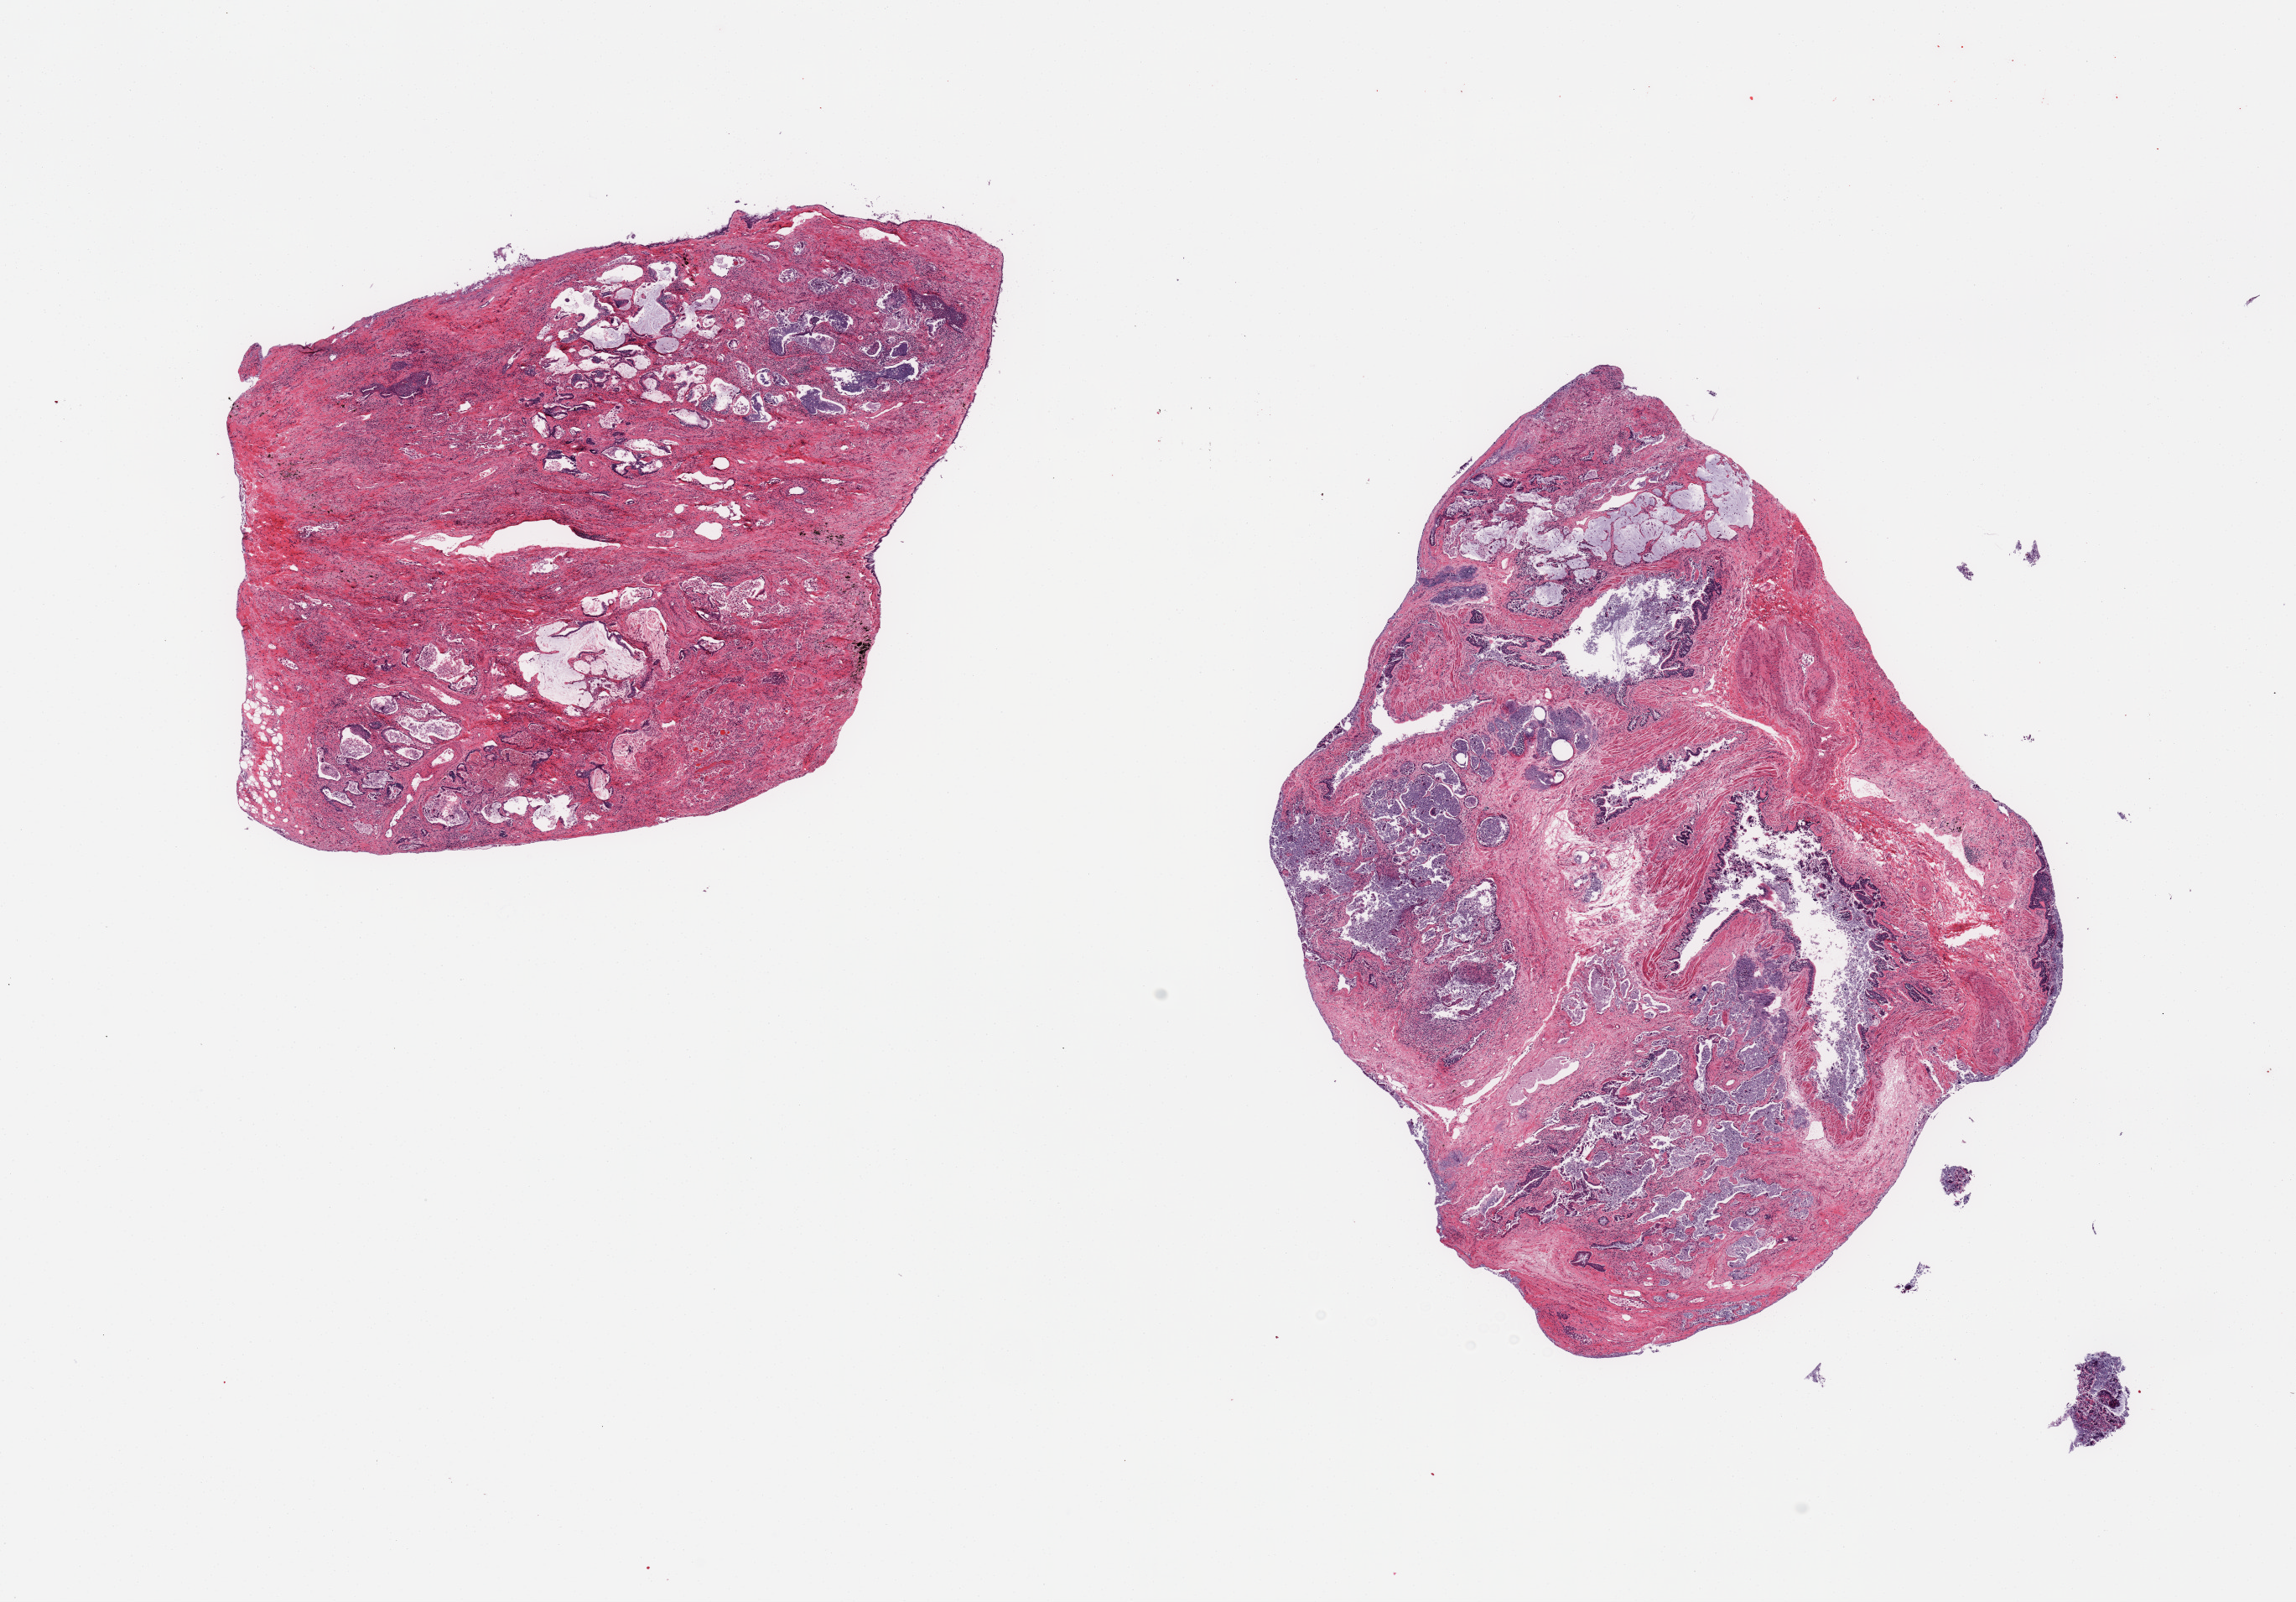
Haematoxylin and eosin whole-slide image, a low-resolution overview of the entire scanned area, about 21.7 x 15.1 mm (acquisition: 20x scan). PAXgene-fixed paraffin-embedded (PFPE) section. Section of lung (target tissue). Donor tissue sample. Donor sex: male.
• review note (as recorded): 2 pieces; severe fibrosis & bronchiectasis; no normal lung tissue